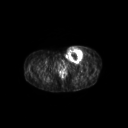
FDG PET of an extremity soft-tissue mass (from a PET/CT study), one axial slice. Slice 59 of 267 in the series (ordered by position). 128 × 128 image matrix, field of view 600 × 600 mm. Patient: female, 24 years. From the clinical record (not read from this slice): histological type: leiomyosarcoma; grade: high; site of the primary tumour: groin.
Annotated regions visible in this slice (expert contour drawn on MRI and transferred to this co-registered scan by the dataset authors):
- gross tumour volume including surrounding oedema: bounding box <64,45,88,64> (left, top, right, bottom; pixels)
- gross tumour volume (mass): <65,46,84,63>